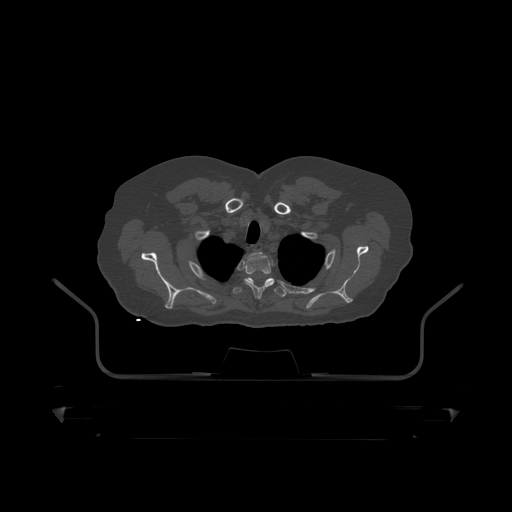
CT including the spine, one axial slice; slice 371 of 390 in the series (ordered by position); 120 kVp; bone window (W 1800 / L 400 HU); 1.25 mm slice thickness; 512 × 512 image matrix, field of view 650 × 650 mm. Male patient, age 60 years. From the clinical record (not read from this slice): primary cancer: prostate.
Structures marked on this image (semi-automatic segmentation, software-assisted and operator-edited):
- T1 vertebra: box from (x=241, y=261) to (x=245, y=268) px
- T2 vertebra: (x=245, y=255)–(x=275, y=299)
- T3 vertebra: (x=233, y=278)–(x=287, y=298)